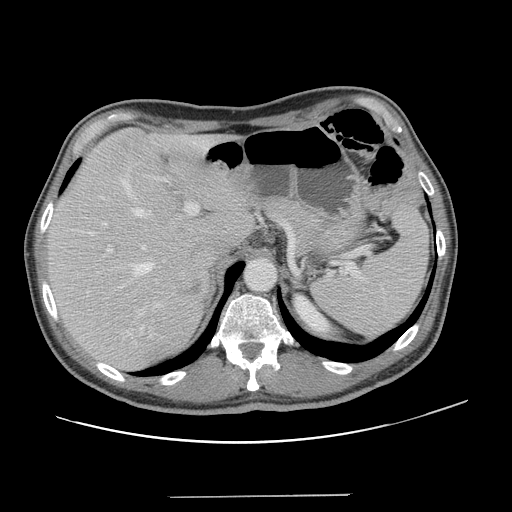
Contrast-enhanced abdominal CT, one axial slice; position 94 of 131 along the scan axis; 120 kVp; soft-tissue window (W 400 / L 40 HU); 512 × 512 image matrix. Male patient, age 60 years. Case-level facts recorded for this patient, not image findings: diagnosis: colorectal cancer liver metastases, imaged before liver resection; multiple liver metastases: no; largest metastasis: 2.5 cm; disease in both lobes: no.
Structures marked on this image (expert manual segmentation):
- hepatic veins: bounding box [x1, y1, x2, y2] px = [94, 179, 155, 330]
- liver: [47, 129, 251, 371]
- planned liver remnant (the part of the liver to remain after resection): [47, 129, 251, 354]
- portal vein (with intrahepatic branches): [101, 144, 205, 280]
- liver metastasis: [182, 280, 204, 296]